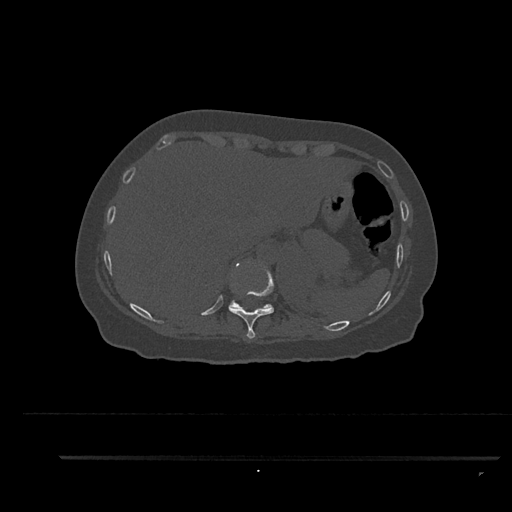
CT including the spine, one axial slice; slice 349 of 797 in the series (ordered by position); 120 kVp; bone window (W 1800 / L 400 HU); 0.5 mm slice thickness; 512 × 512 image matrix, field of view 408 × 408 mm. Patient: female, 44 years. From the clinical record (not read from this slice): primary cancer: renal; vertebrae with lytic lesions (as recorded): L1.
Outlined on this slice (semi-automatic segmentation, software-assisted and operator-edited):
- T10 vertebra: bounding box <228,261,274,339> (left, top, right, bottom; pixels)
- T11 vertebra: <229,285,273,309>